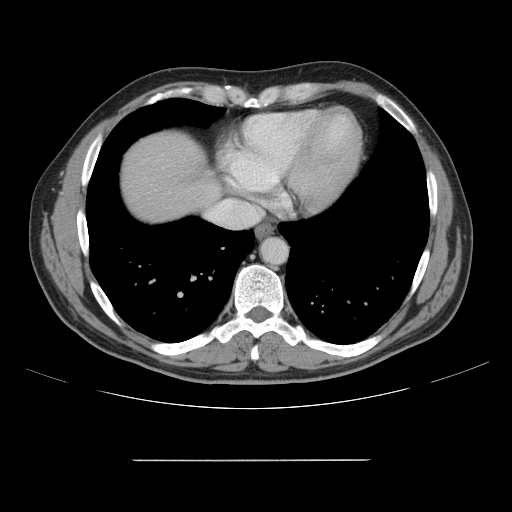
Contrast-enhanced abdominal CT, one axial slice. Position 145 of 164 along the scan axis. Intravenous contrast given. Soft-tissue window (W 400 / L 40 HU). 2.5 mm slice thickness. 512 × 512 image matrix, field of view 404 × 404 mm. Male patient, age 54 years. From the clinical record (not read from this slice): diagnosis: colorectal cancer liver metastases, imaged before liver resection; multiple liver metastases: yes; largest metastasis: 1 cm; chemotherapy before resection: yes.
Outlined on this slice (outlined manually by an expert reader):
- hepatic veins: box from (x=208, y=199) to (x=258, y=224) px
- liver: (x=121, y=132)–(x=218, y=220)
- planned liver remnant (the part of the liver to remain after resection): (x=122, y=132)–(x=220, y=221)